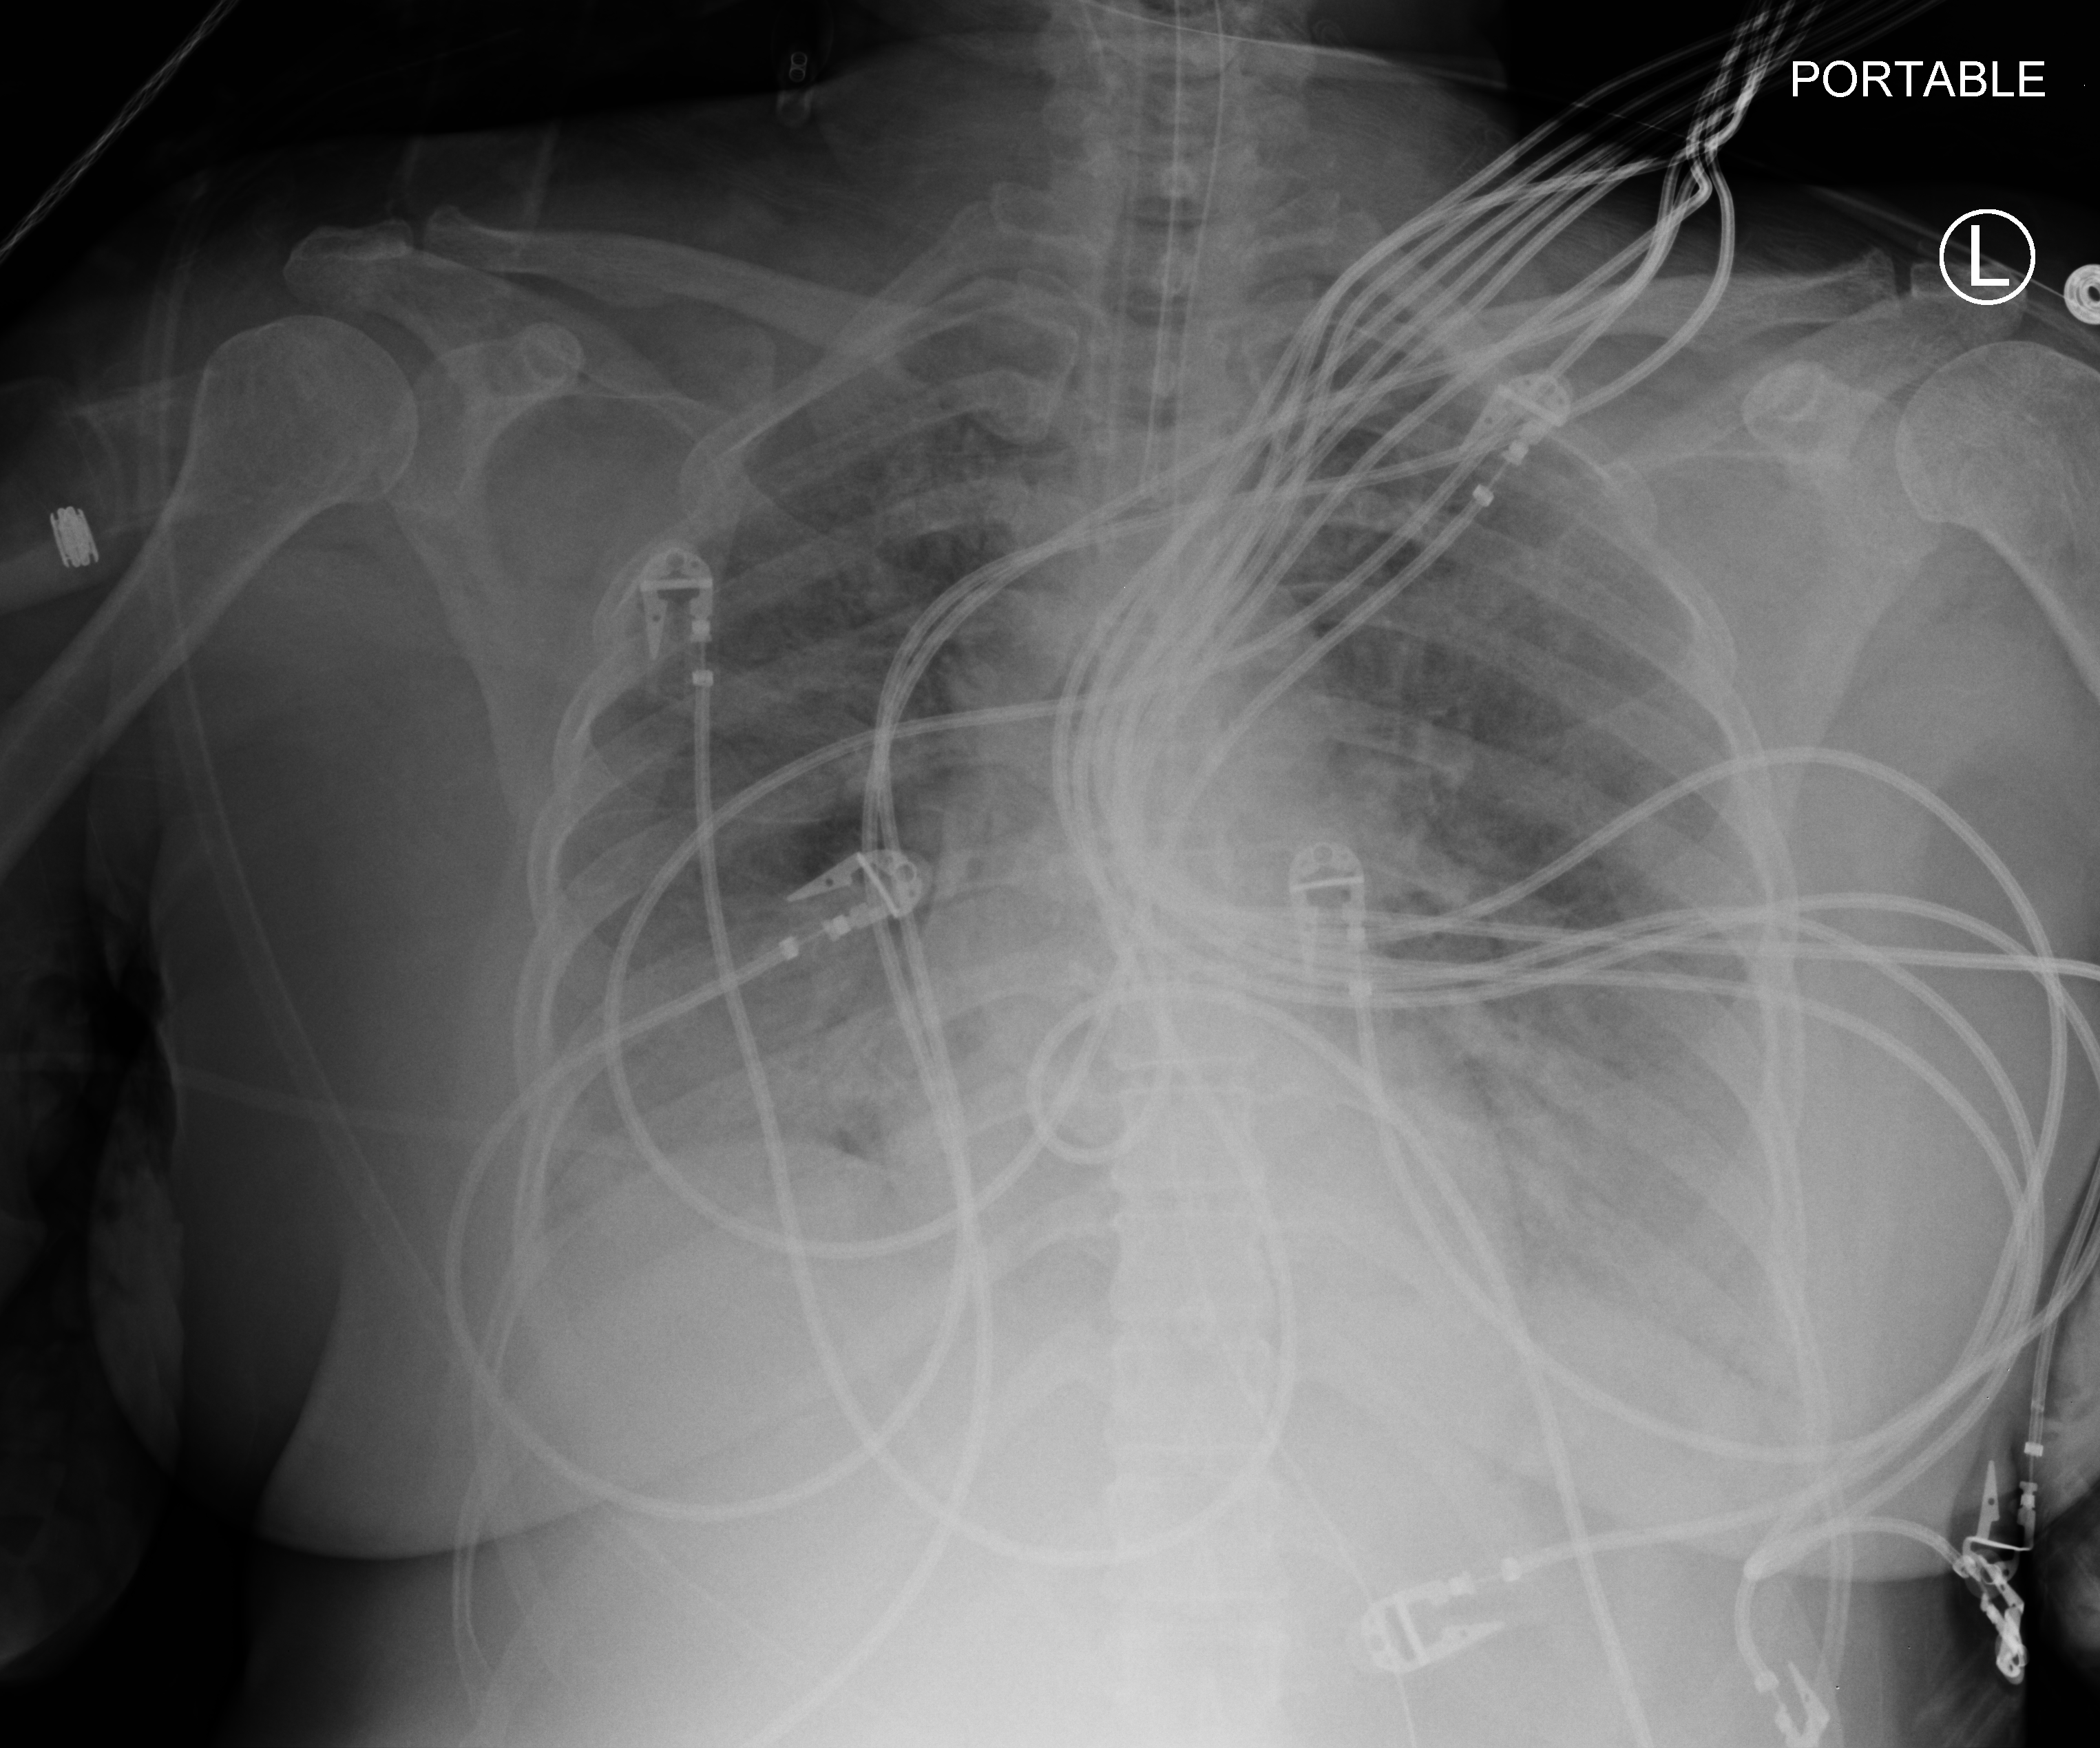
Chest X-ray (portable); anteroposterior (AP) projection. Patient hospitalised with COVID-19; male, aged 18–59 years.
From the hospital-stay record, not from the radiograph (when in the stay this image was taken is not recorded): mechanically ventilated during this hospital stay: yes; smoking status (admission record): never; admitted to intensive care during this hospital stay: yes.